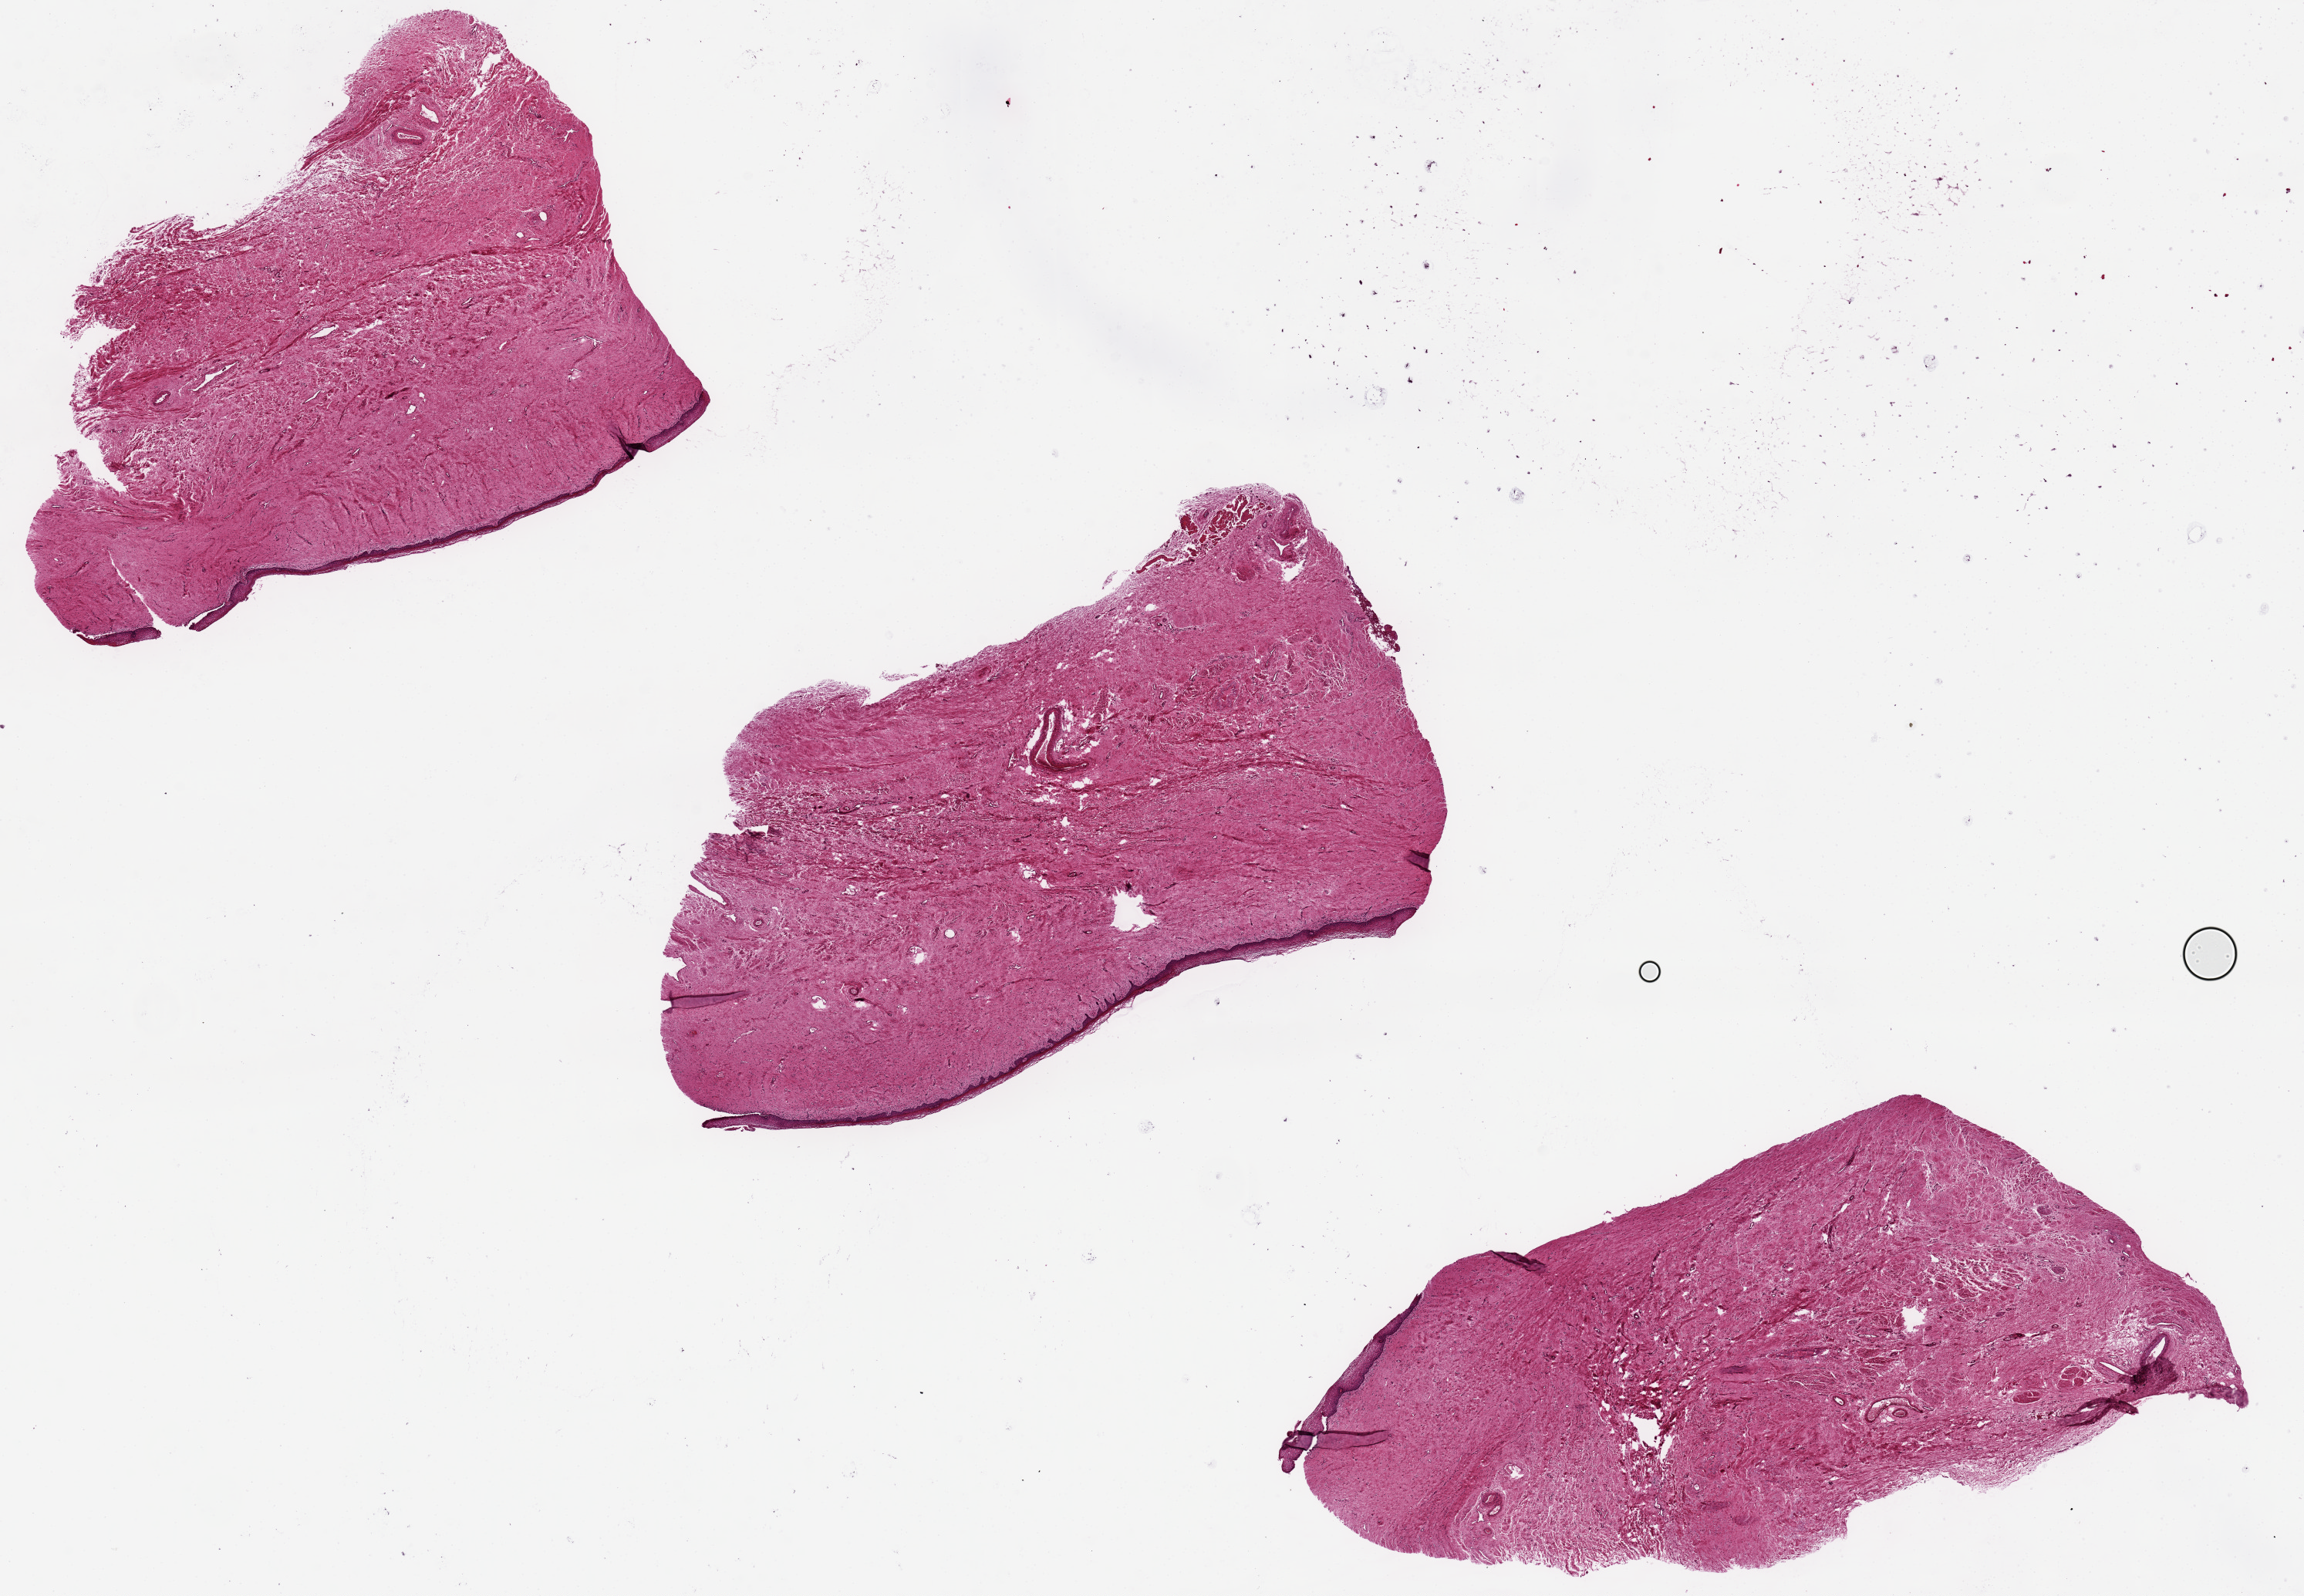
H&E whole-slide image — low-resolution overview of the scanned area, about 23.6 x 16.4 mm, PAXgene-fixed, paraffin-embedded tissue, section of vagina (target tissue), tissue donor sample. Donor: female.
• review note (as recorded): 0; epithelium varies in quantity